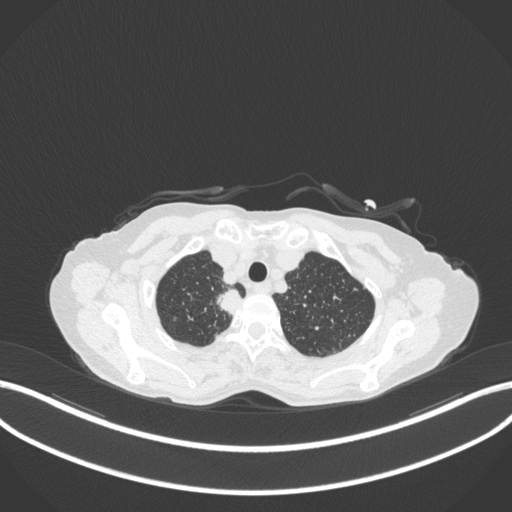
Chest CT, one axial slice; position 324 of 363 along the scan axis; reconstruction kernel B31f; lung window (W 1500 / L -600 HU); 1 mm slice thickness; 512 × 512 image matrix. Patient: female, 75 years. Case-level facts recorded for this patient, not image findings: clinical TNM (as recorded): T1c N1 M1.
Outlined on this slice (bounding box drawn by a radiologist):
- lung tumour (recorded histology: adenocarcinoma): bounding box <213,286,247,318> (left, top, right, bottom; pixels)